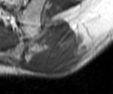
MRI of an extremity soft-tissue mass, one axial slice; MR volume resampled by the dataset authors to the PET/CT grid (not the native acquisition matrix); 3.27 mm slice thickness; 113 × 94 image matrix, field of view 110 × 92 mm. Male patient. Case-level facts recorded for this patient, not image findings: histological type: leiomyosarcoma; grade: intermediate; site of the primary tumour: left pelvis.
Outlined on this slice (expert contour drawn on MRI and transferred to this co-registered scan by the dataset authors):
- gross tumour volume (mass): bounding box [x1, y1, x2, y2] px = [22, 18, 84, 74]